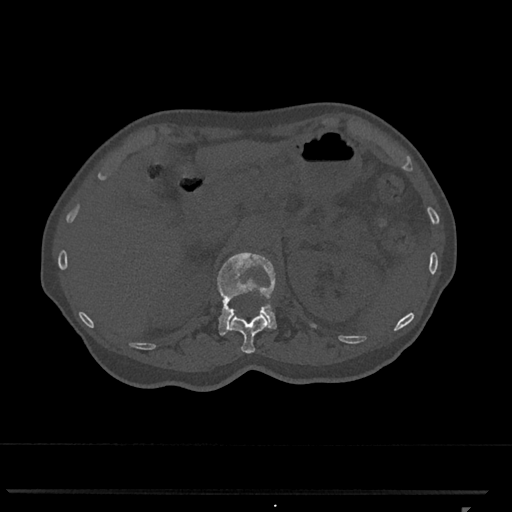
CT including the spine, one axial slice. Position 431 of 793 along the scan axis. Reconstruction kernel Br40s/3. Bone window (W 1800 / L 400 HU). 0.5 mm slice thickness. 512 × 512 image matrix, field of view 380 × 380 mm. Patient: female, 62 years. From the clinical record (not read from this slice): primary cancer: renal.
Structures marked on this image (semi-automatic segmentation, software-assisted and operator-edited):
- L1 vertebra: bounding box <217,252,277,336> (left, top, right, bottom; pixels)
- T12 vertebra: <229,312,269,354>